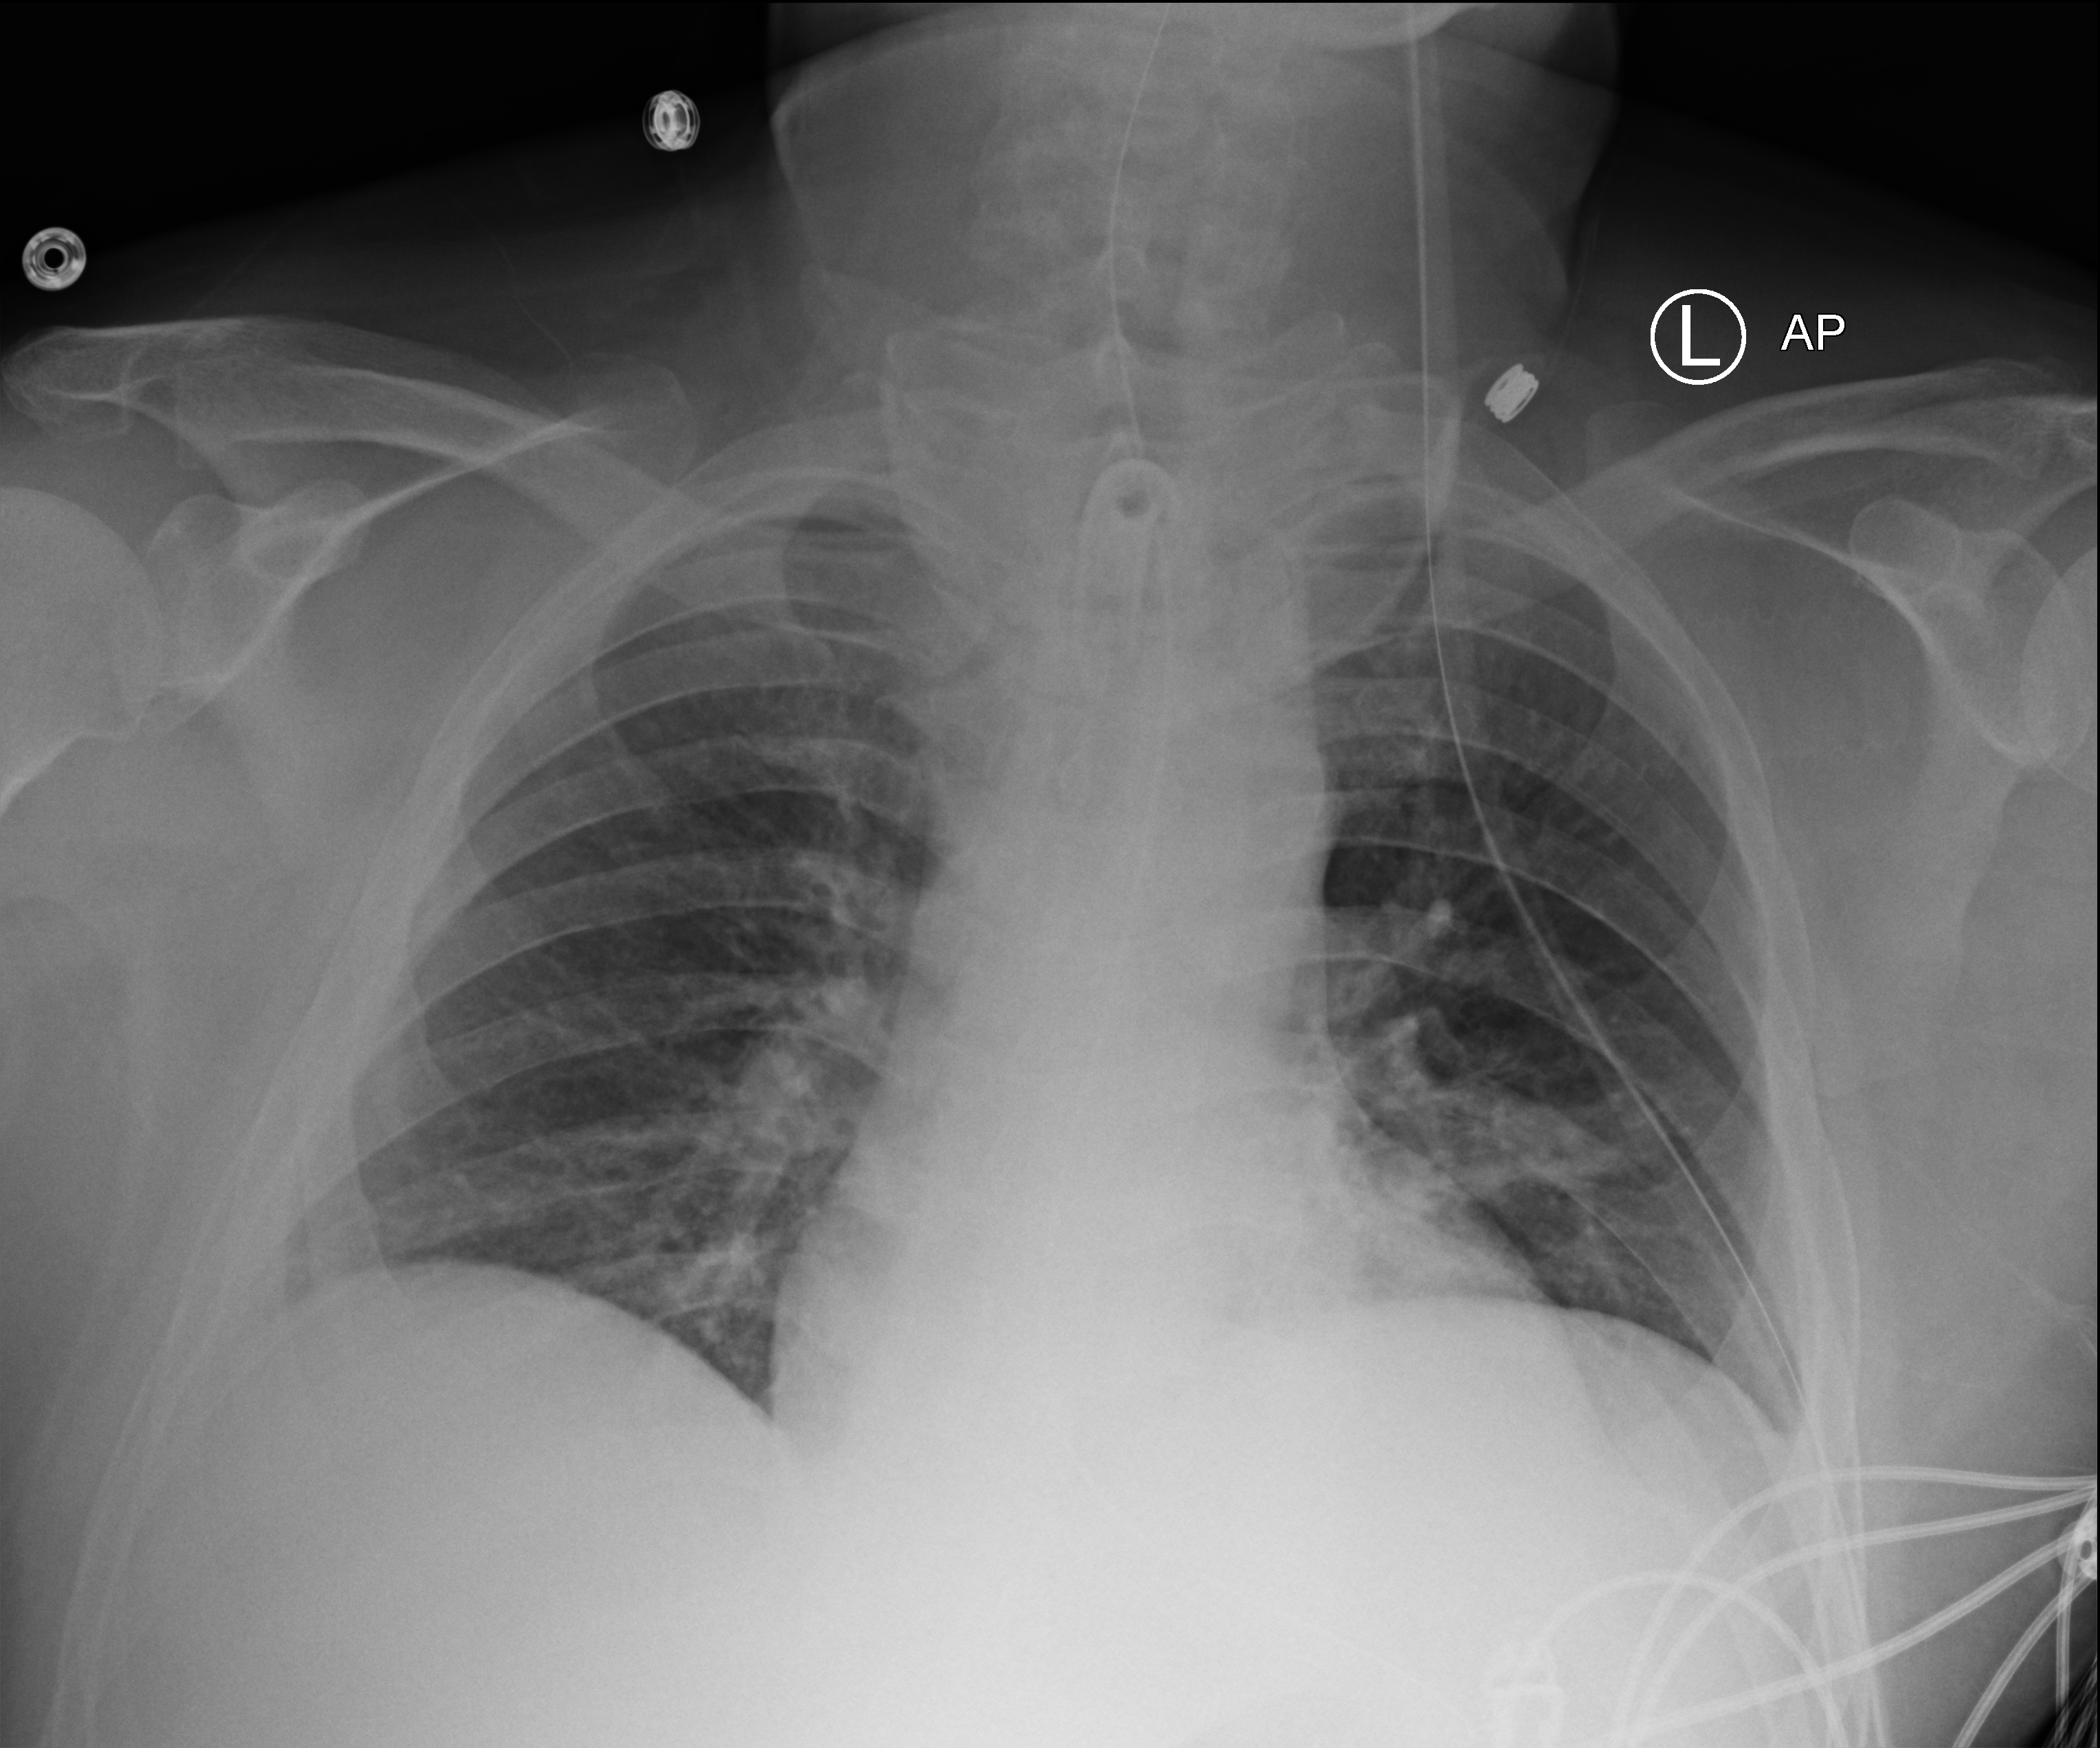
Bedside chest radiograph (computed radiography), anteroposterior (AP) projection. Male patient hospitalised with COVID-19, age 18–59 years.
Hospital-stay facts (about this admission, not read from this image; timing relative to this image not recorded): length of hospital stay: 65 days.